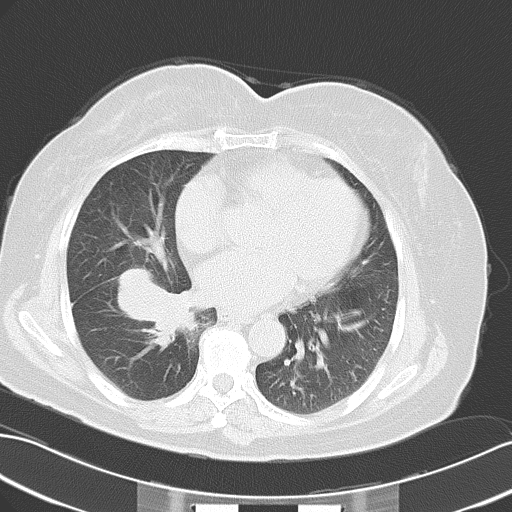
Chest CT, one axial slice; slice 23 of 50 in the series (ordered by position); reconstruction kernel B70f; lung window (W 1500 / L -600 HU); 512 × 512 image matrix. Patient: female, 63 years. Case-level facts recorded for this patient, not image findings: clinical TNM (as recorded): T3 N0 M0.
Annotated regions visible in this slice (bounding box drawn by a radiologist):
- lung tumour (recorded histology: adenocarcinoma): bounding box [x1, y1, x2, y2] px = [117, 268, 198, 348]